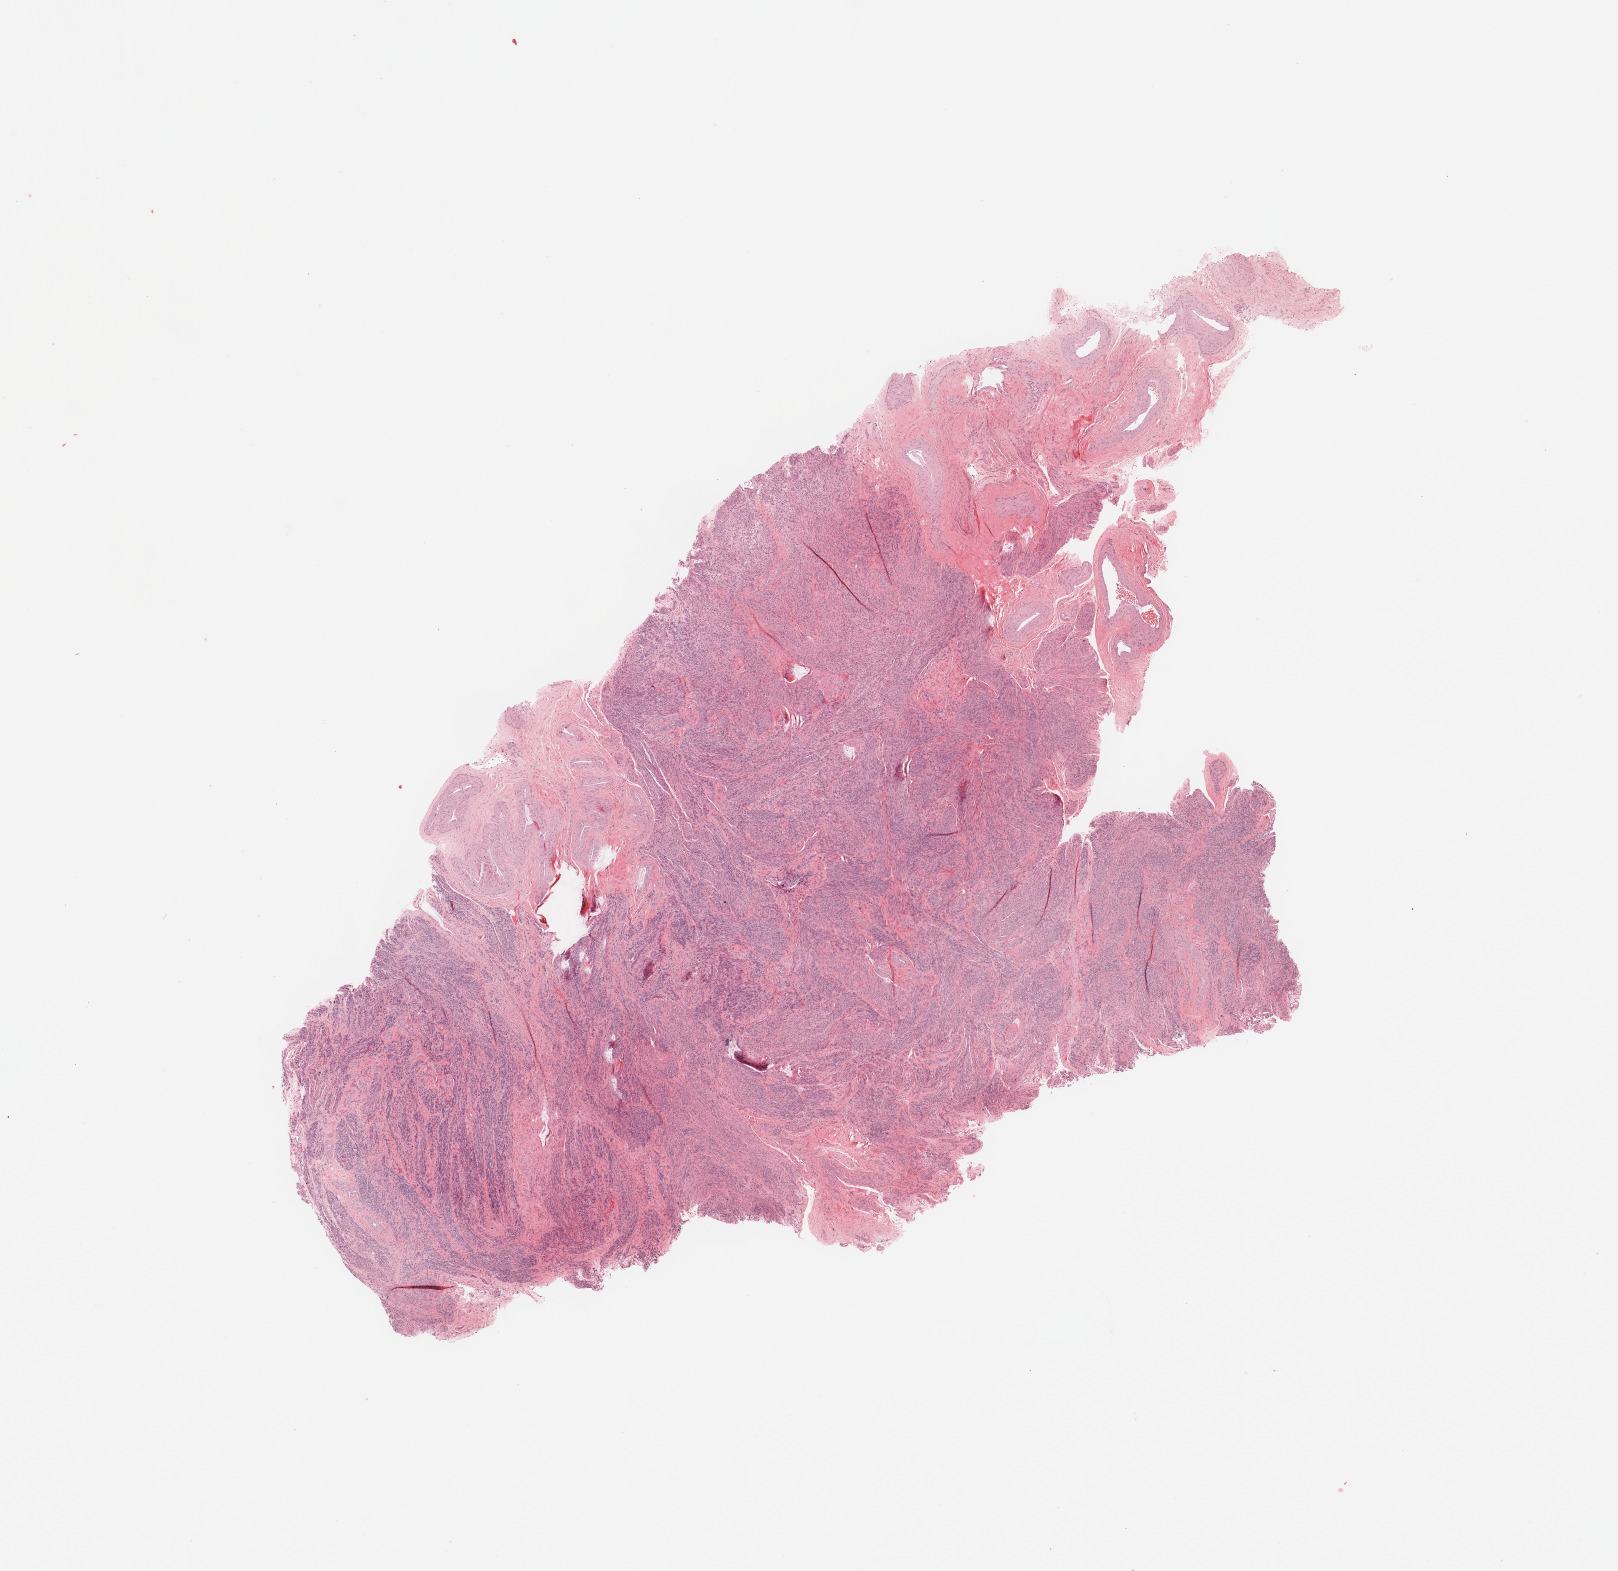
H&E-stained whole-slide image — whole scanned area (about 12.8 x 12.4 mm, acquisition: 20x scan) shown as a low-resolution overview. Normal (non-tumour) tissue sample, uterus. 70-year-old female patient.
- this section: normal (non-tumour) tissue from the same patient
- patient diagnosis (cohort enrolment): corpus endometrial carcinoma (uterus)